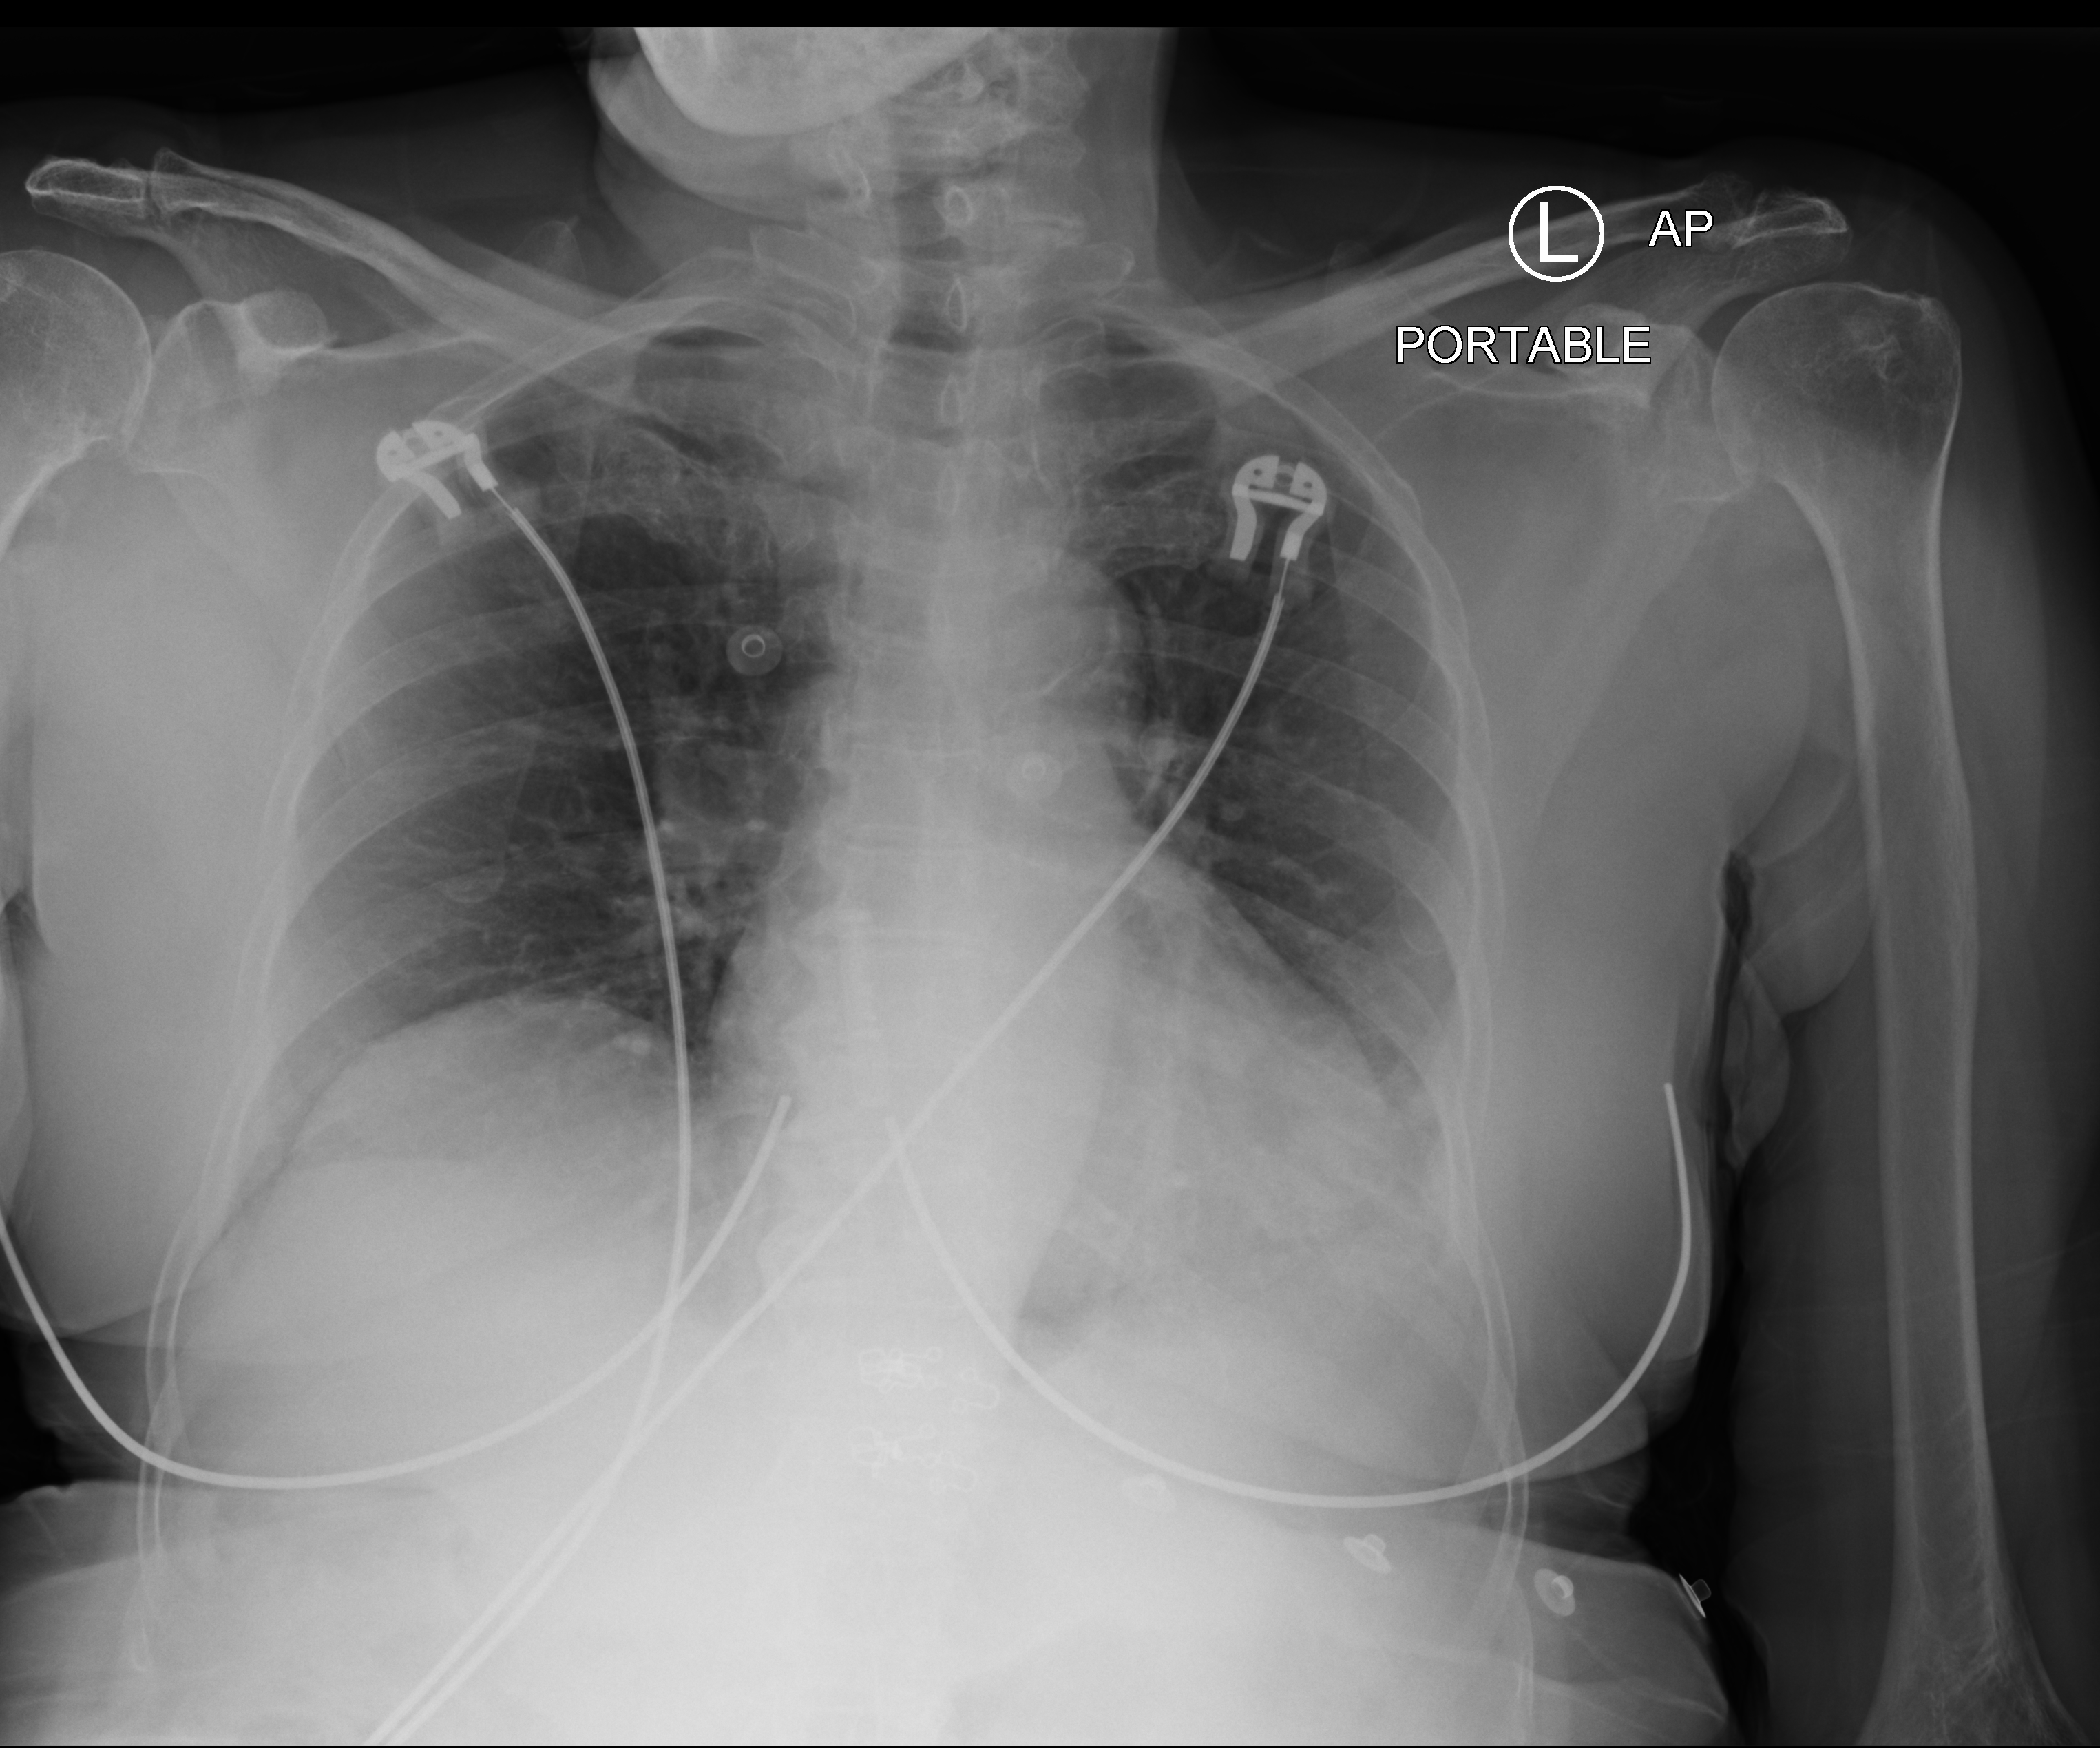
Bedside chest radiograph (computed radiography), anteroposterior (AP) projection. Patient hospitalised with COVID-19; female, aged 75–90 years.
Admission-level facts for this patient (not findings on this image; timing relative to this image not recorded): hypertension (admission record): yes; admitted to intensive care during this hospital stay: no; mechanically ventilated during this hospital stay: no.